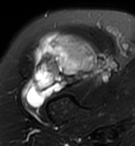
MRI of an extremity soft-tissue mass, one axial slice. Slice 73 of 95 in the series (ordered by position). T2-weighted fat-saturated. MR volume resampled by the dataset authors to the PET/CT grid (not the native acquisition matrix). 3.27 mm slice thickness. 135 × 146 image matrix. Female patient. From the clinical record (not read from this slice): histological type: pleiomorphic undifferentiated sarcoma; grade: high; site of the primary tumour: right quadricep.
Annotated regions visible in this slice (expert contour drawn on MRI and transferred to this co-registered scan by the dataset authors):
- gross tumour volume including surrounding oedema: bounding box (x1, y1, x2, y2) in pixels: (23, 31, 99, 108)
- gross tumour volume (mass): (23, 31, 99, 108)